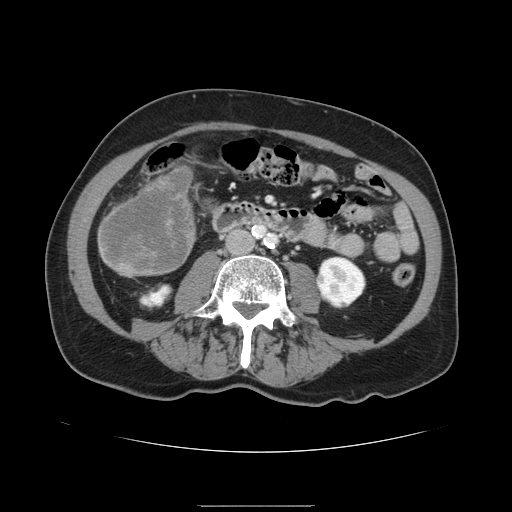
Contrast-enhanced abdominal CT, one axial slice. Slice 27 of 168 in the series (ordered by position). 120 kVp. Intravenous contrast given. Soft-tissue window (W 400 / L 40 HU). 512 × 512 image matrix, field of view 386 × 386 mm. Male patient, age 74 years. From the clinical record (not read from this slice): diagnosis: colorectal cancer liver metastases, imaged before liver resection; multiple liver metastases: no; largest metastasis: 14.5 cm; disease in both lobes: yes.
Annotated regions visible in this slice (manually delineated by an expert):
- liver: box from (x=97, y=167) to (x=196, y=277) px
- liver metastasis: (x=101, y=172)–(x=192, y=274)